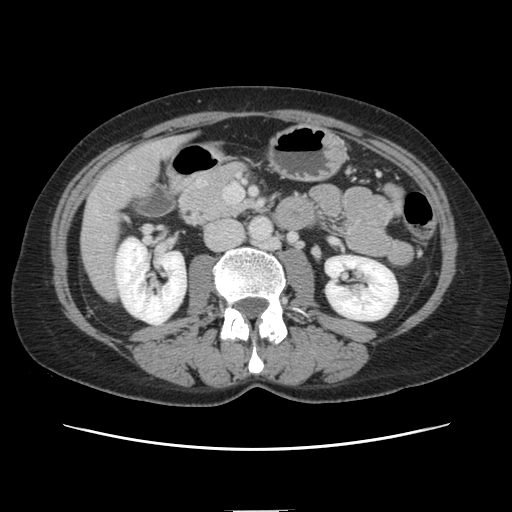
Contrast-enhanced abdominal CT, one axial slice; position 42 of 141 along the scan axis; 120 kVp; intravenous contrast given; soft-tissue window (W 400 / L 40 HU); 2.5 mm slice thickness; 512 × 512 image matrix, field of view 350 × 350 mm. Female patient, age 63 years. Case-level facts recorded for this patient, not image findings: diagnosis: colorectal cancer liver metastases, imaged before liver resection; multiple liver metastases: yes; largest metastasis: 3.2 cm; disease in both lobes: yes.
Annotated regions visible in this slice (manually delineated by an expert):
- liver: bounding box [x1, y1, x2, y2] px = [82, 138, 187, 299]